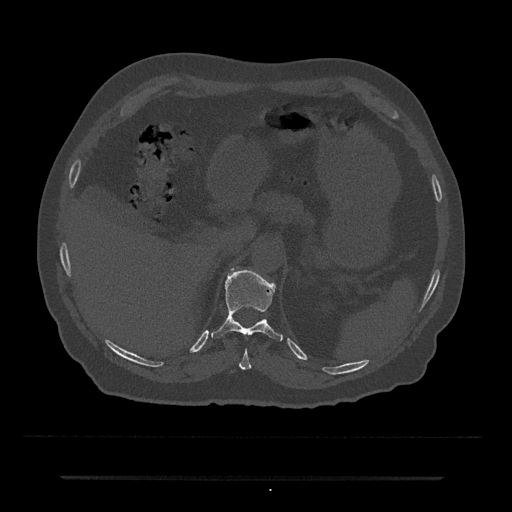
CT including the spine, one axial slice; slice 183 of 797 in the series (ordered by position); reconstruction kernel Br40s/3; bone window (W 1800 / L 400 HU); 0.5 mm slice thickness; 512 × 512 image matrix, field of view 437 × 437 mm. Patient: male, 69 years. Case-level facts recorded for this patient, not image findings: primary cancer: prostate.
Annotated regions visible in this slice (semi-automatic segmentation, software-assisted and operator-edited):
- T10 vertebra: bounding box <239,349,252,370> (left, top, right, bottom; pixels)
- T11 vertebra: <211,268,283,342>